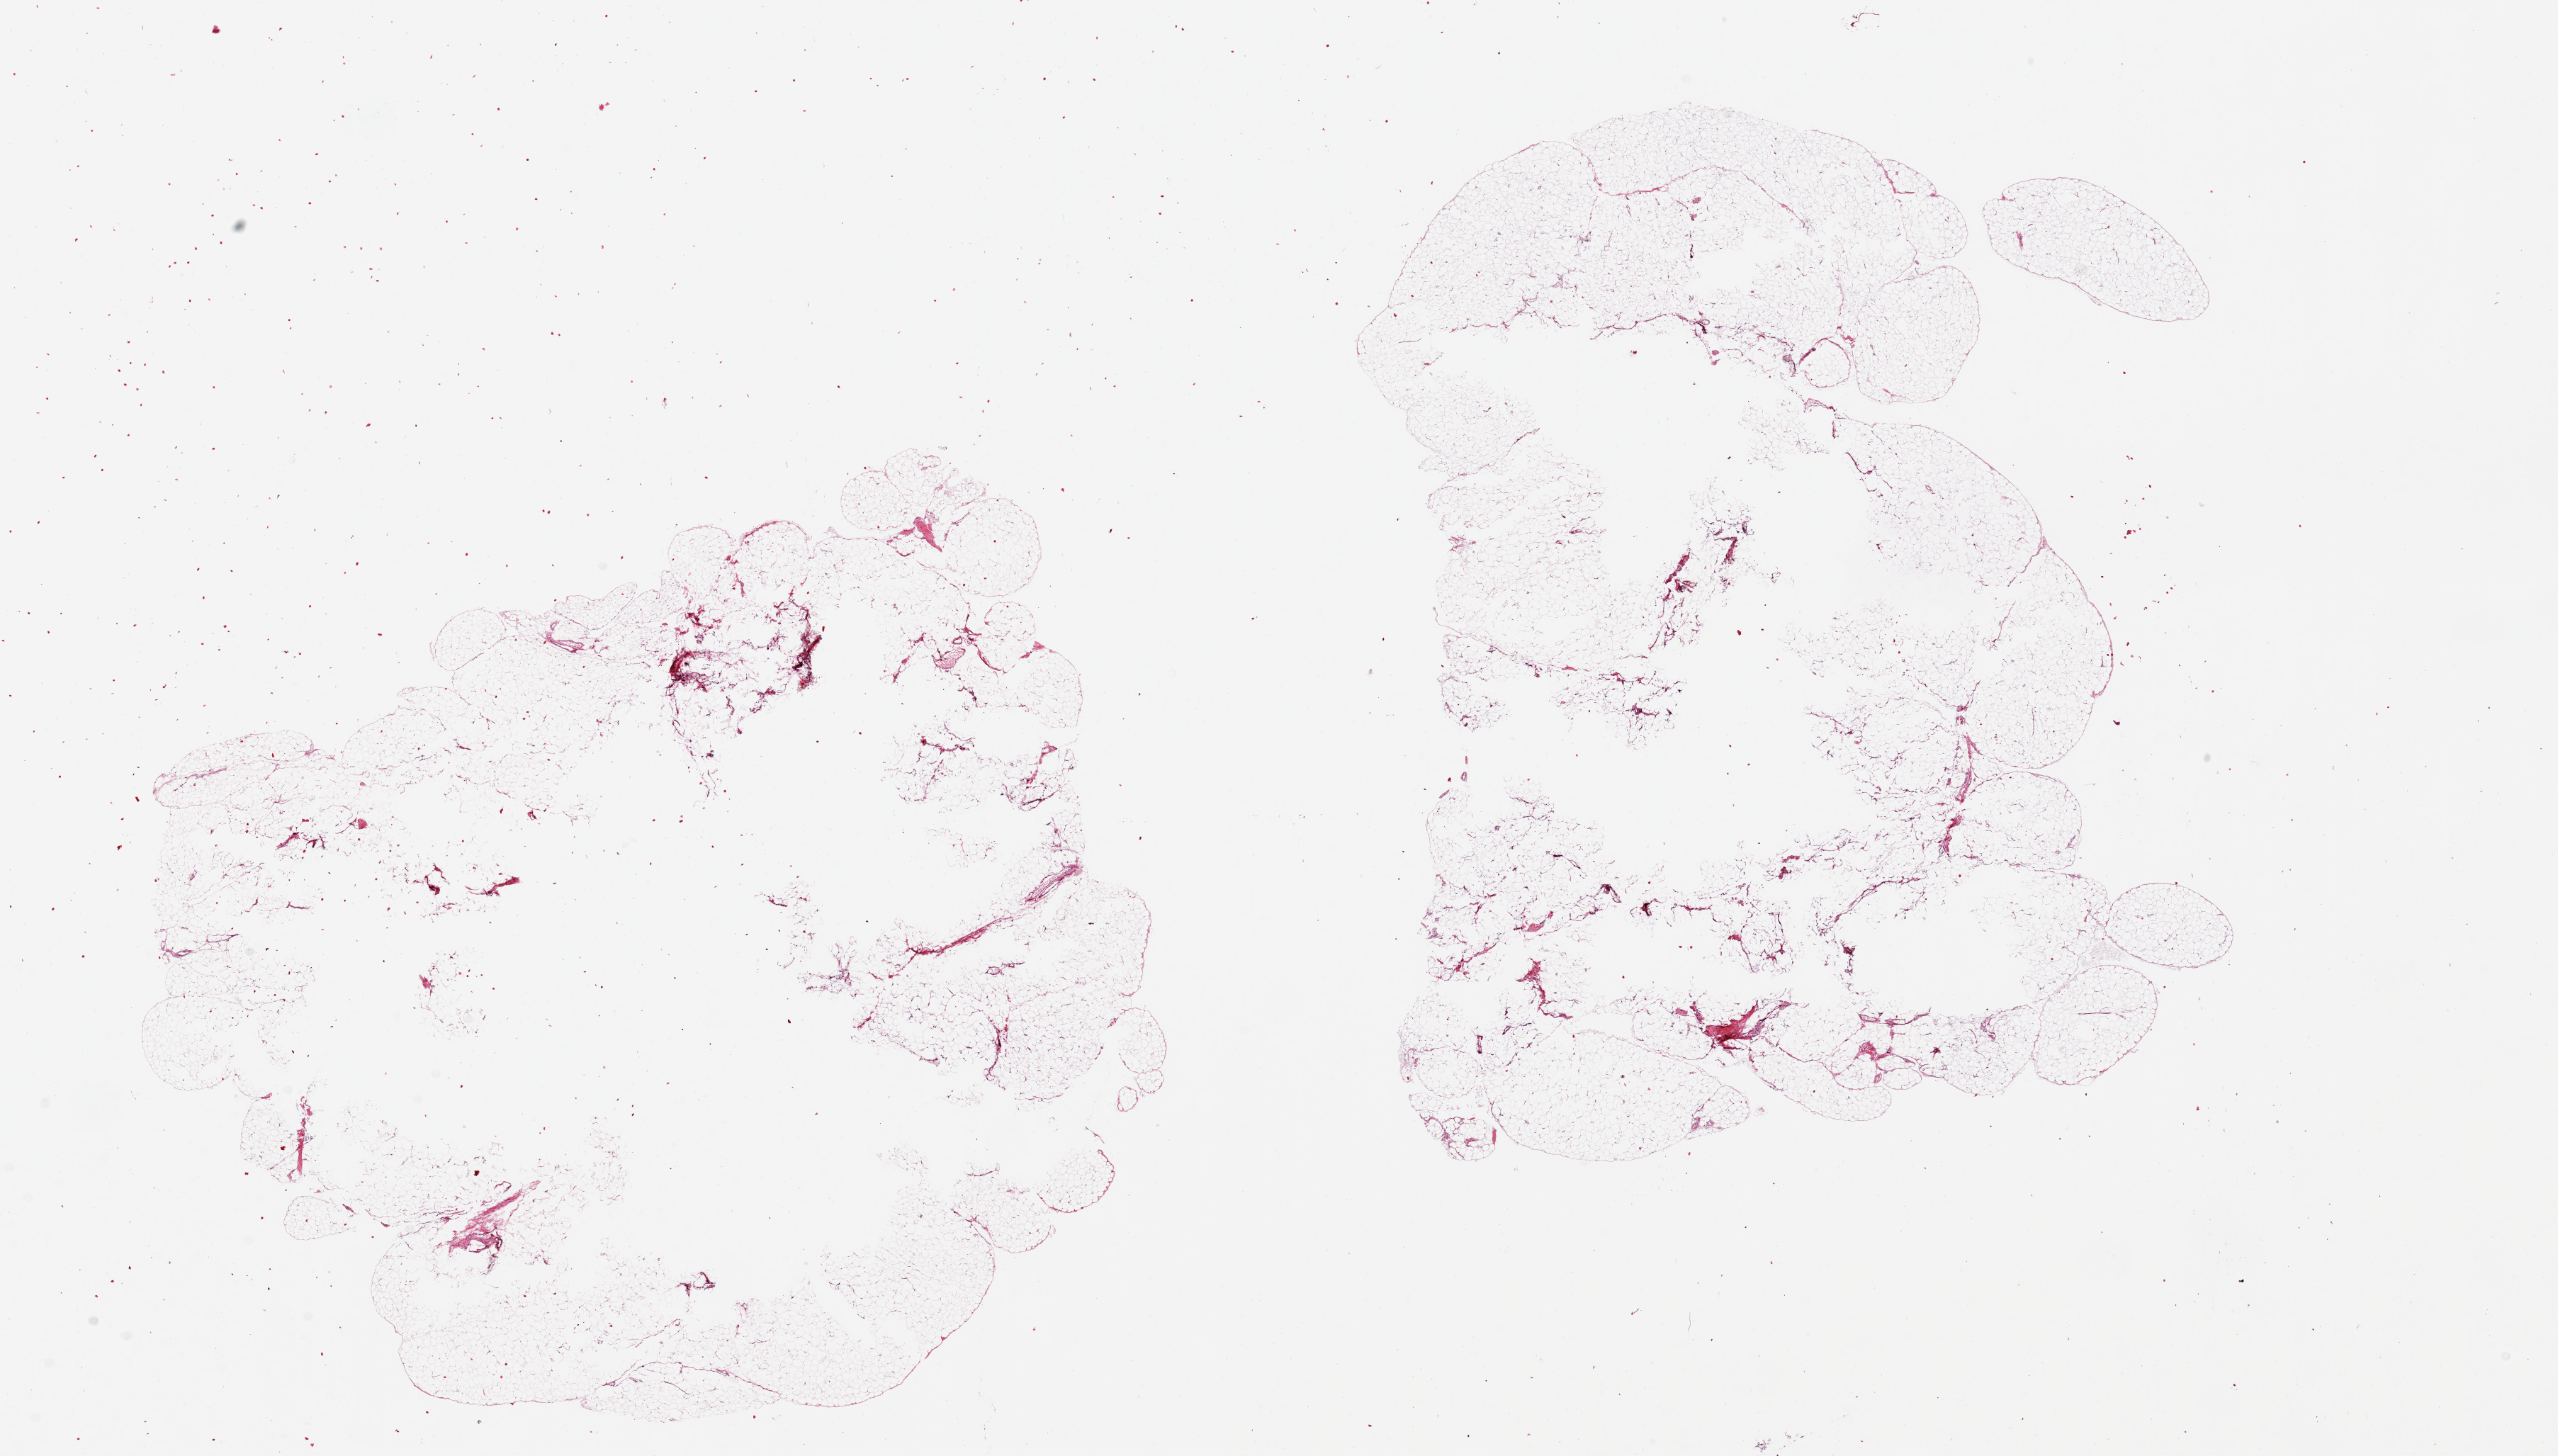
Hematoxylin and eosin (H&E) whole-slide image — whole scanned area (about 28.5 x 16.3 mm) shown as a low-resolution overview; PAXgene-fixed, paraffin-embedded tissue; section of omentum (target tissue); donor tissue sample. Donor: female.
Review note (as recorded): 2 pieces, 11.5x10 & 11x9.5mm.